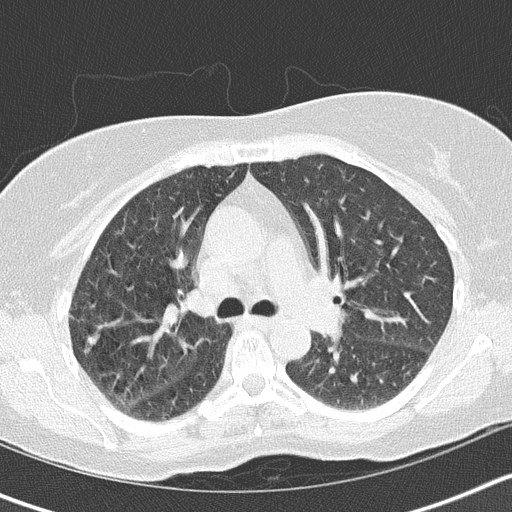
Chest CT (low-dose screening protocol), one axial image, baseline screening round, lung window (W 1500 / L -600 HU), 2 mm slice thickness, 120 kVp, slice 53 of 148 in the series. Female, age 61 years at enrolment.
• Expert reader's lesion annotation, box from (x=68, y=321) to (x=113, y=366) px.
• No non-calcified nodule or mass ≥4 mm was recorded by the screening reader at this exam.
• Official screen result: negative screen, minor abnormalities not suspicious for lung cancer.
• Participant outcome: lung cancer diagnosed 486 days after this screen (after the second annual screen) — small cell carcinoma, NOS, right upper lobe, stage IIIA (AJCC 6th edition), 7 mm at pathology.